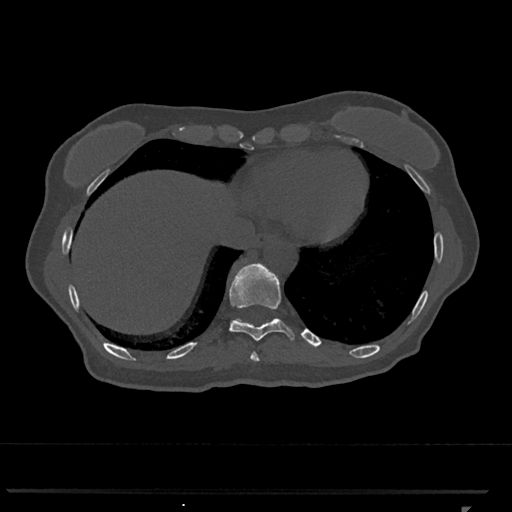
CT including the spine, one axial slice; slice 566 of 793 in the series (ordered by position); reconstruction kernel Br40s/3; 120 kVp; bone window (W 1800 / L 400 HU); 0.5 mm slice thickness; 512 × 512 image matrix. Patient: female, 62 years. From the clinical record (not read from this slice): primary cancer: renal.
Outlined on this slice (semi-automatically segmented with operator editing):
- T10 vertebra: box from (x=230, y=262) to (x=295, y=341) px
- T11 vertebra: (x=234, y=308)–(x=272, y=321)
- T9 vertebra: (x=251, y=352)–(x=259, y=362)